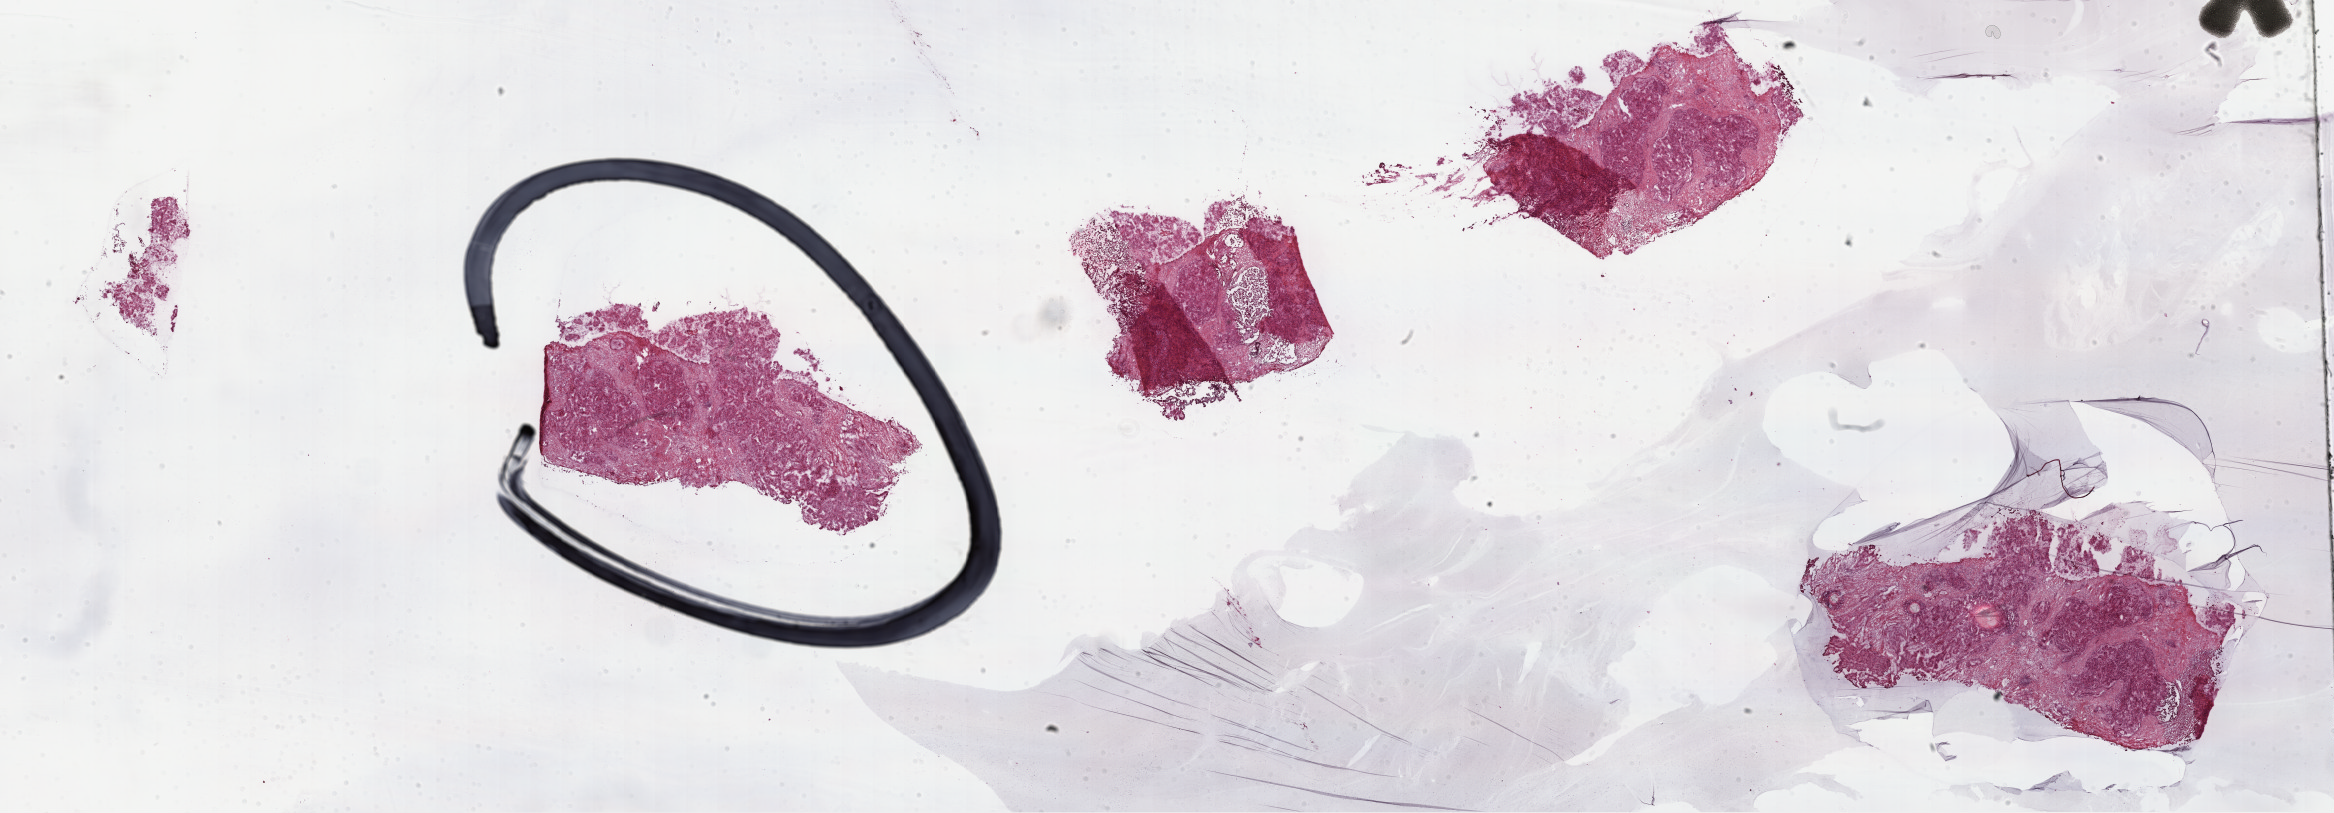
Digitized H&E-stained tissue section (whole slide), shown as a low-resolution overview of the whole scanned area (about 37.8 x 13.2 mm). Frozen section from the top of the tissue portion. Sample: primary tumour, kidney. Female, age 59 years at initial diagnosis. Pathologist review of this section (percent, as recorded): tumour cells 100%, tumour nuclei 60%, normal cells 0%, stromal cells 0%, necrosis 0%. Inflammatory infiltration, as recorded: lymphocyte infiltration 4%, monocyte infiltration 4%, neutrophil infiltration 0%.
Lymph nodes positive (case pathology): 5 of 10 examined. Histologic diagnosis: Papillary adenocarcinoma, NOS. Laterality: left.